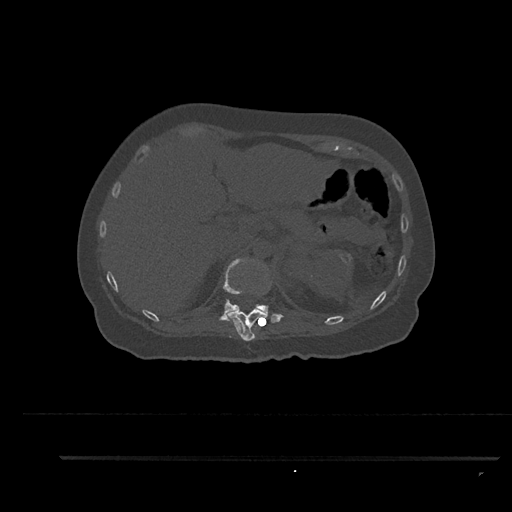
CT including the spine, one axial slice; bone window (W 1800 / L 400 HU); 0.5 mm slice thickness; 512 × 512 image matrix, field of view 408 × 408 mm. Female patient, age 44 years. From the clinical record (not read from this slice): primary cancer: renal.
Structures marked on this image (semi-automatically segmented with operator editing):
- T11 vertebra: box from (x=229, y=293) to (x=267, y=341) px
- T12 vertebra: (x=219, y=258)–(x=284, y=322)